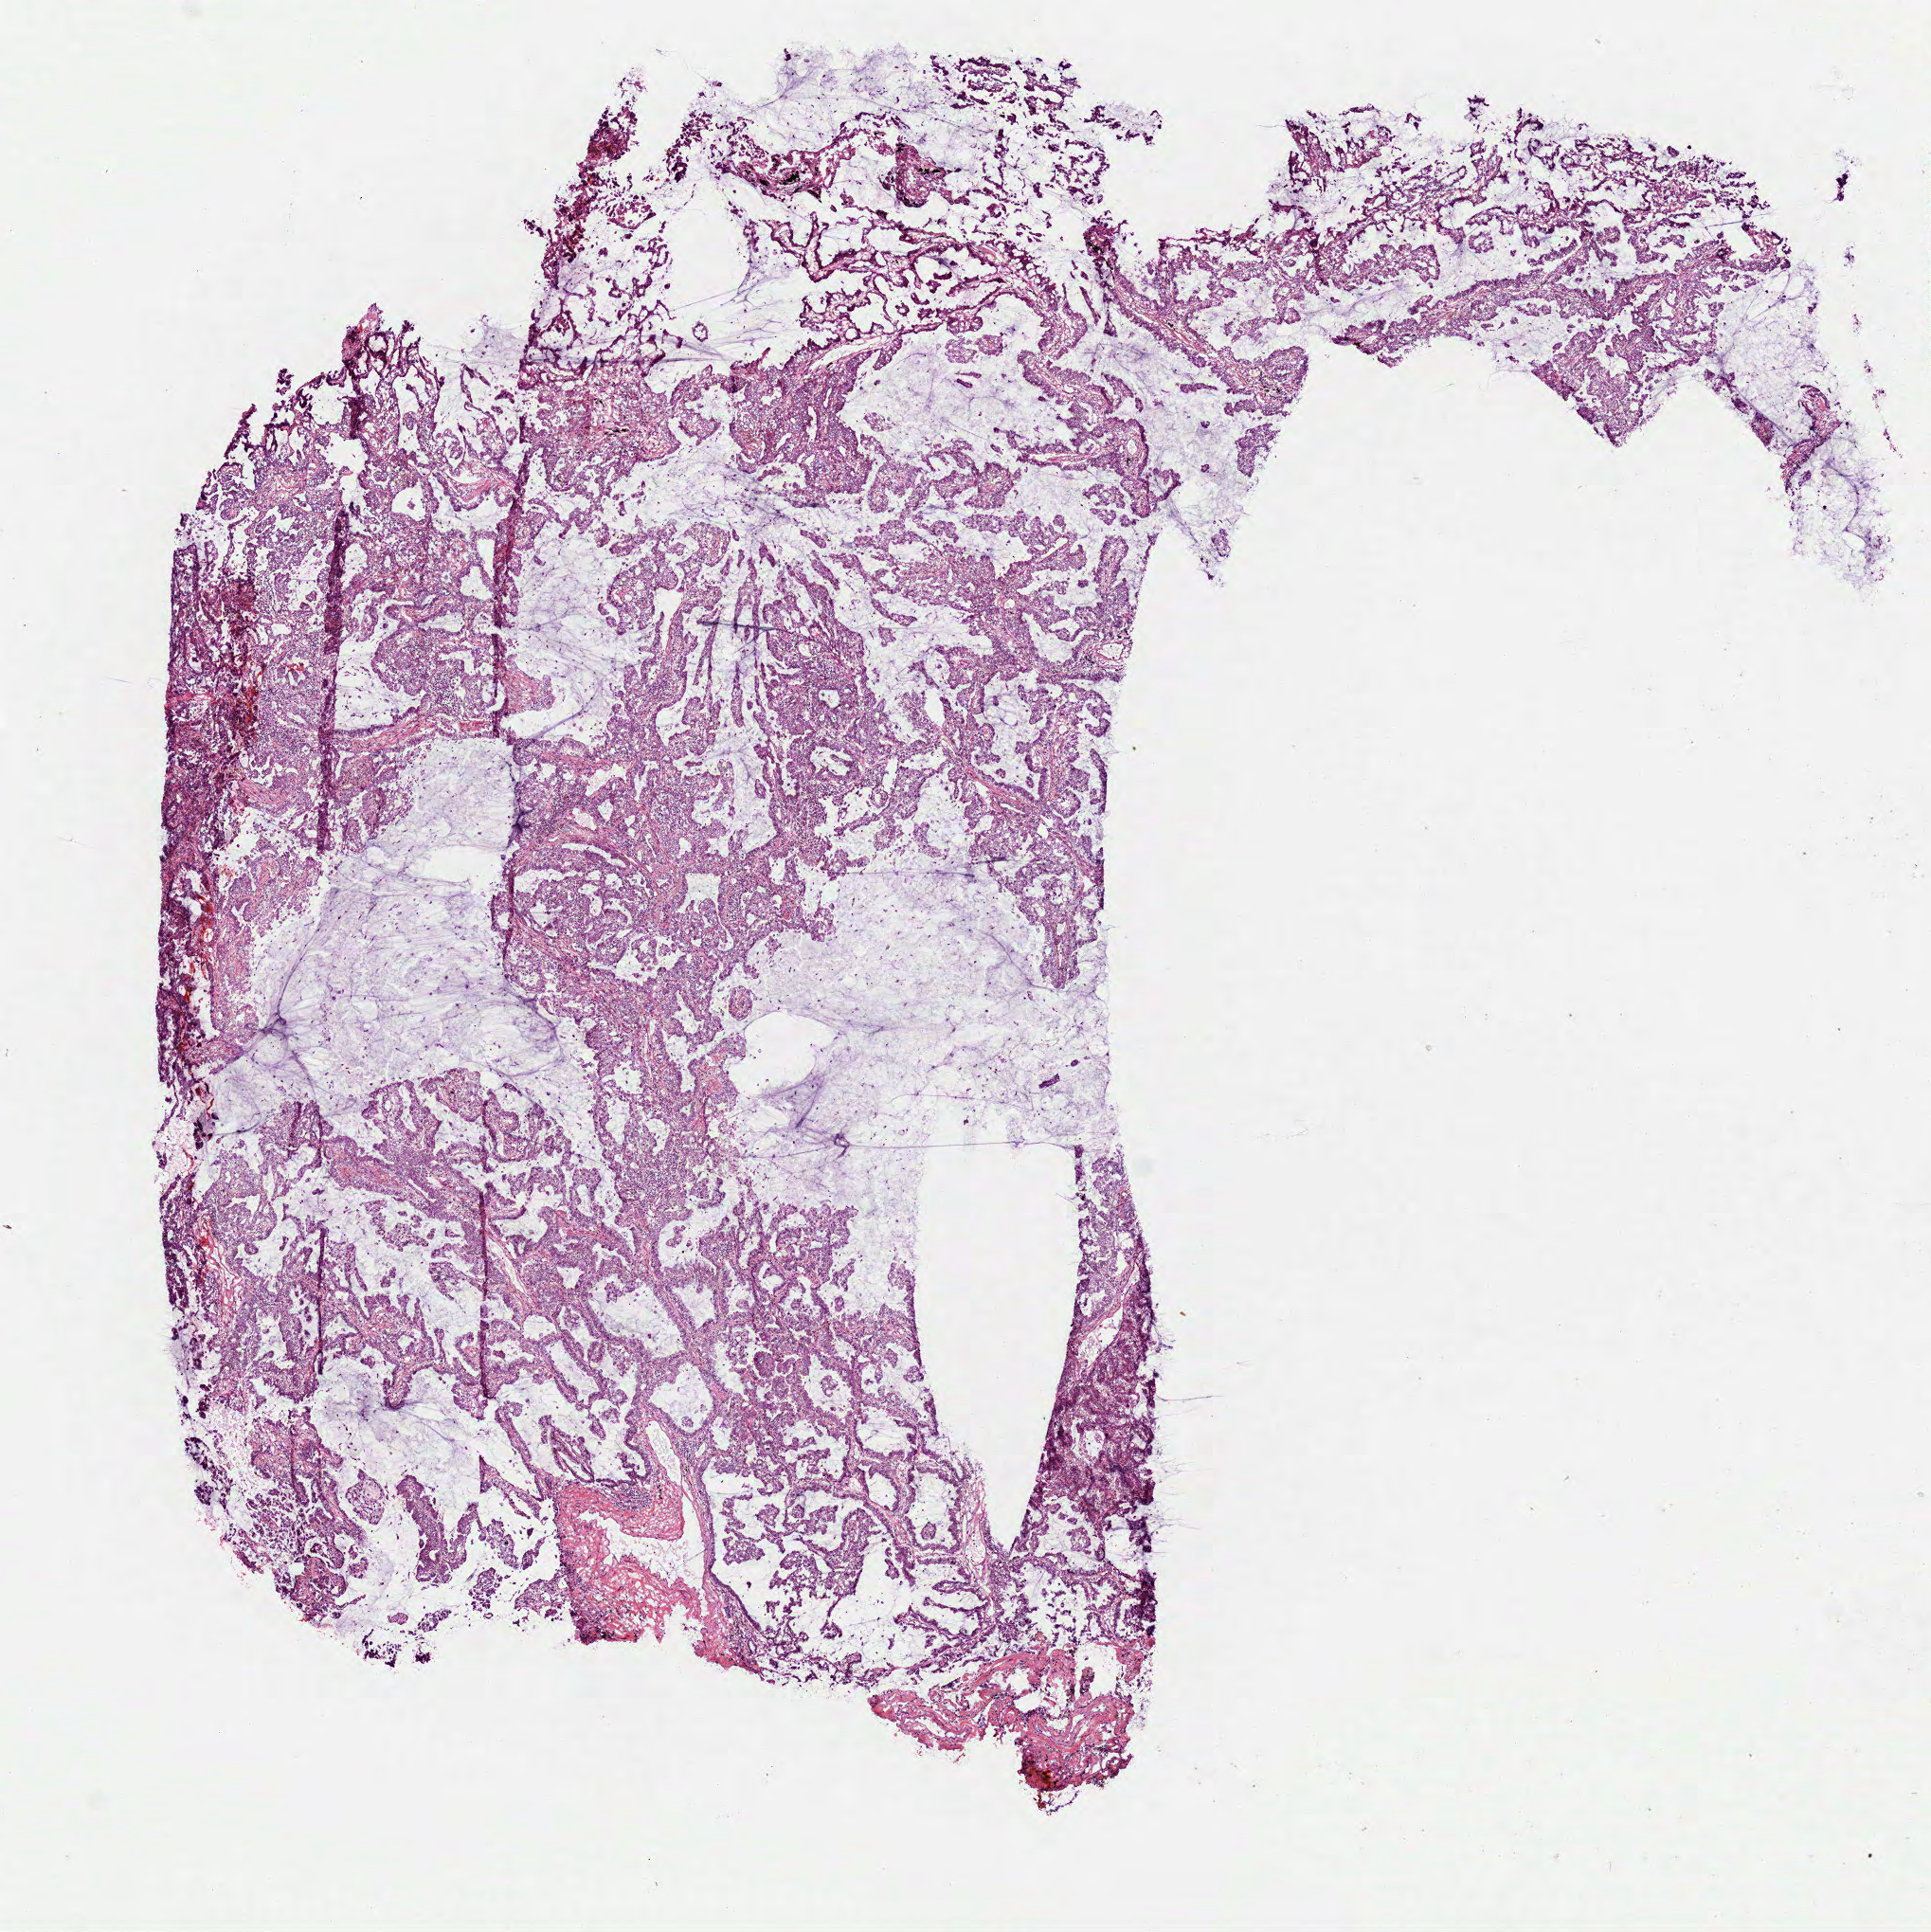
Digitized H&E-stained tissue section (whole slide), whole scanned area (about 8.2 x 8.2 mm) shown as a low-resolution overview, frozen section, primary tumour sample from the lung. Male, age 71 years at initial diagnosis. Pathologist review of this section (percent, as recorded): tumour cells 85%, tumour nuclei 65%, normal cells 0%, stromal cells 15%, necrosis 0%.
Pathologic diagnosis: Adenocarcinoma with mixed subtypes (upper lobe, lung). AJCC pathologic stage: IIB (6th edition). TNM: T2 N1 M0.